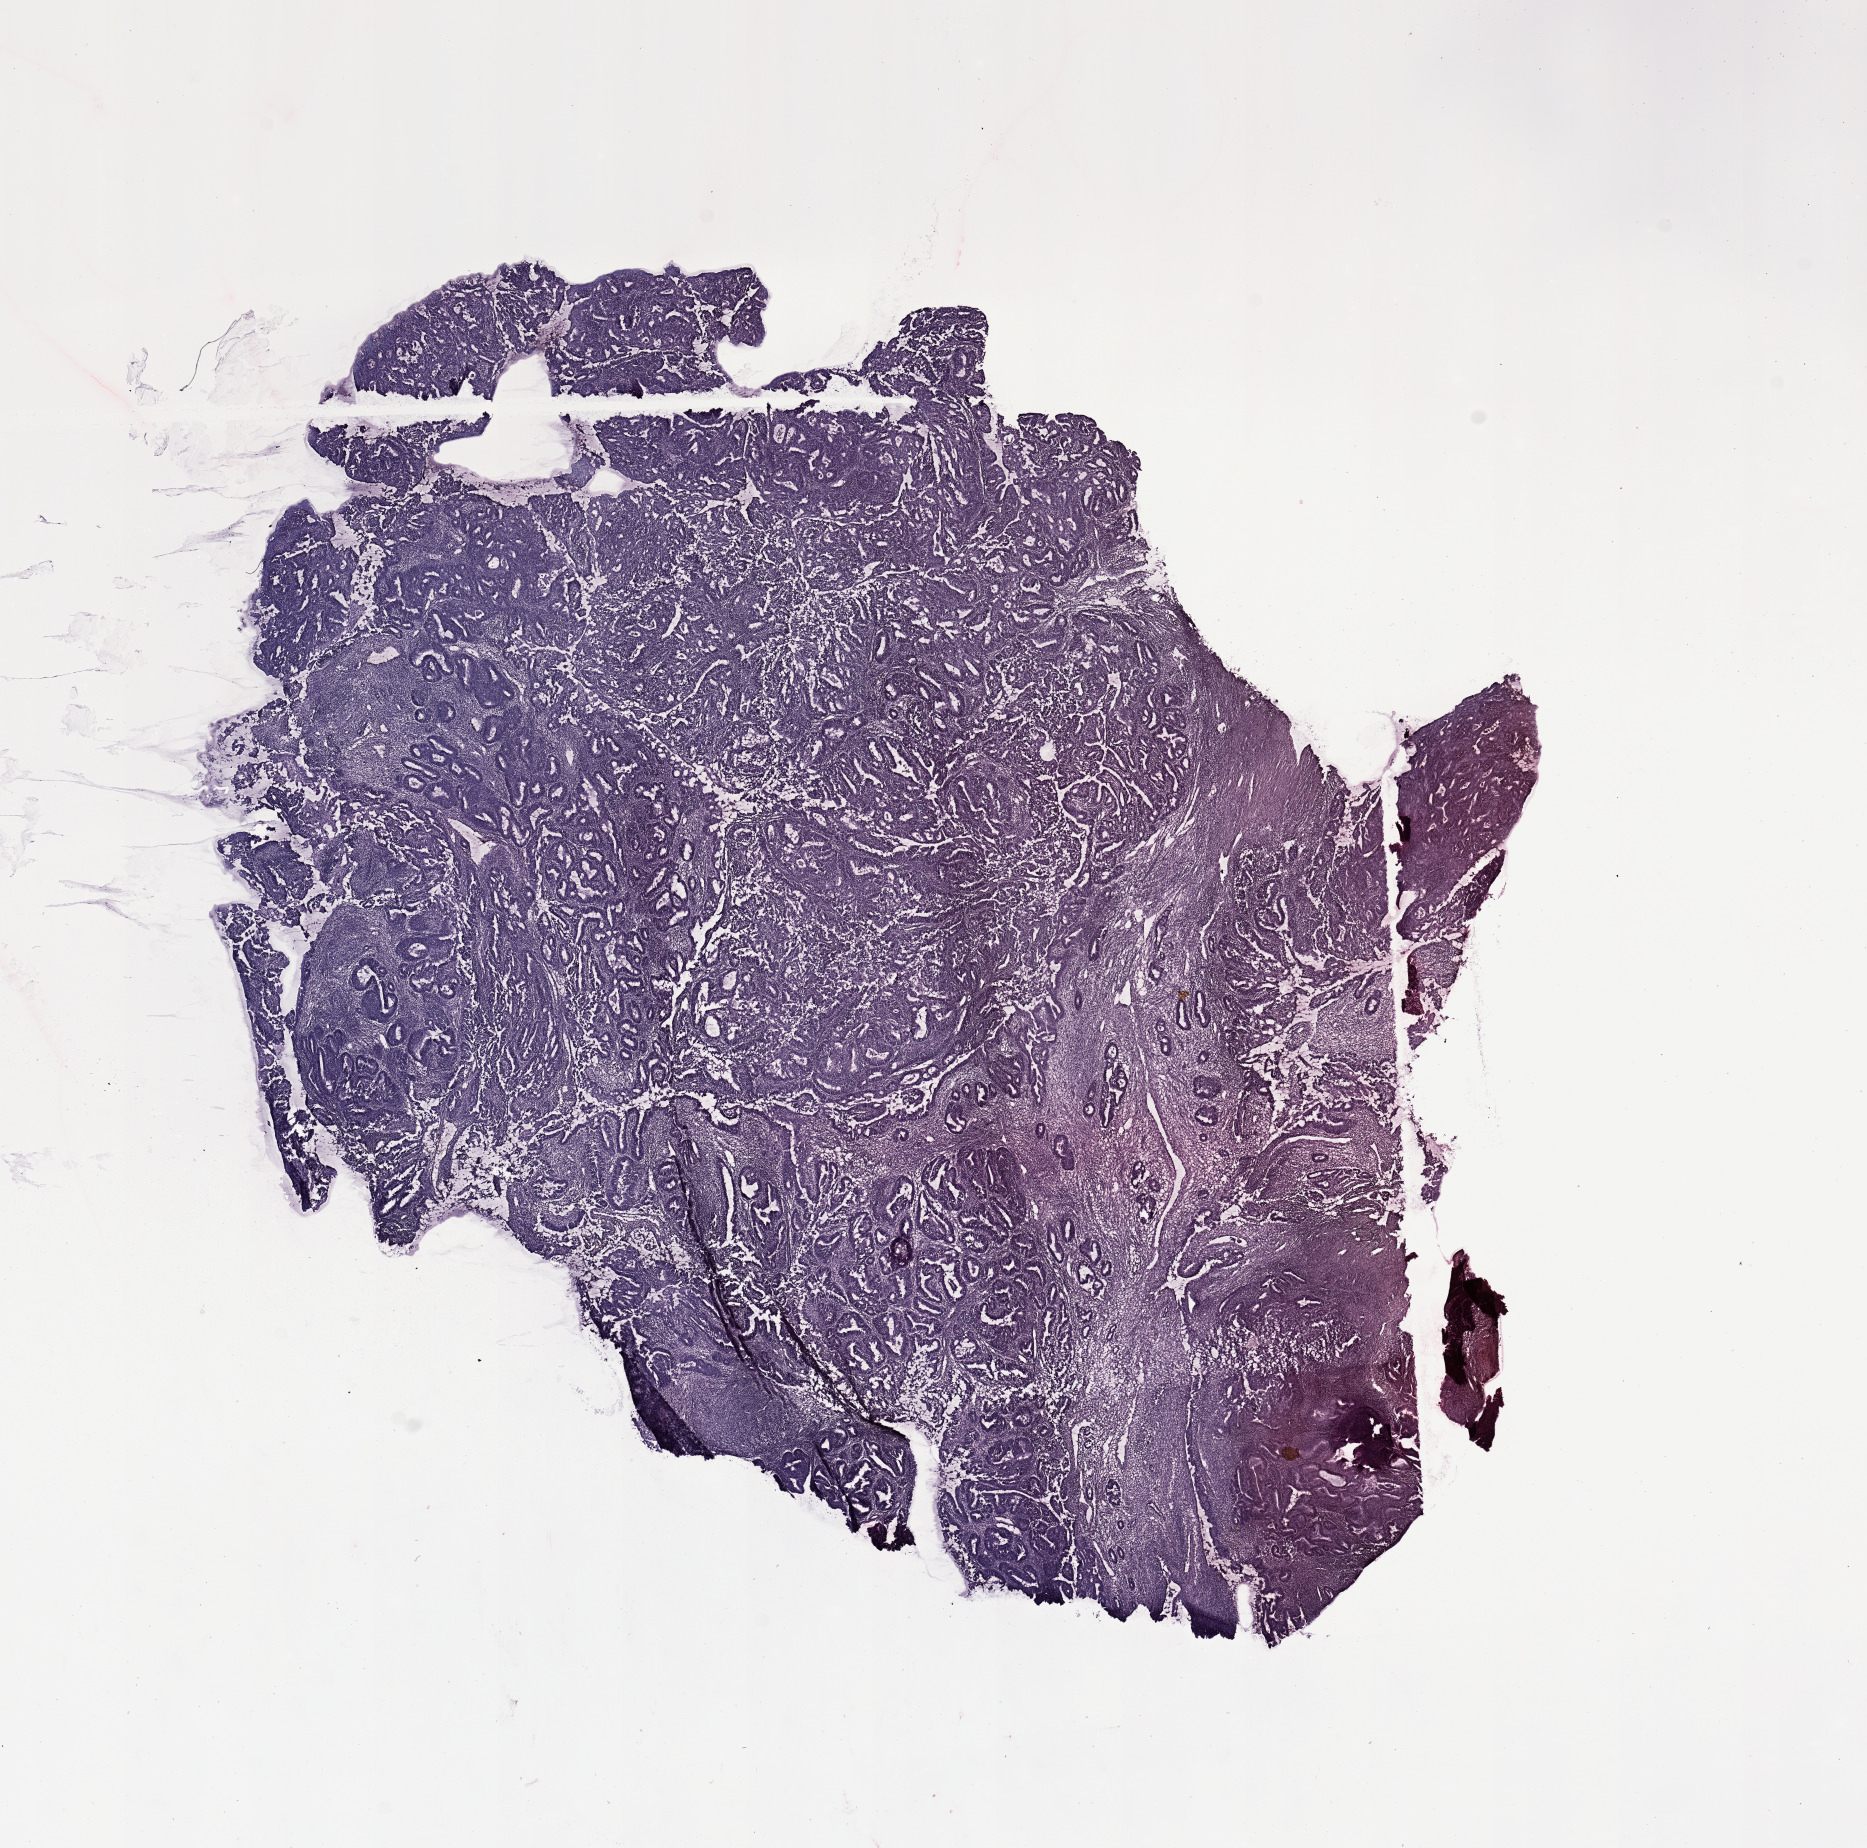
Whole-slide histology image, H&E — whole scanned area (about 14.8 x 14.6 mm, slide scanned at 20x) shown as a low-resolution overview. Tumour tissue sample, sampled site: uterus. Patient: female, age 41 years. Histologic grade: G2 (moderately differentiated). Pathologist review of this section (percent, as recorded): tumour nuclei 90%, necrosis 0%.
Diagnosis: Endometrioid adenocarcinoma, NOS. AJCC pathologic stage: I.